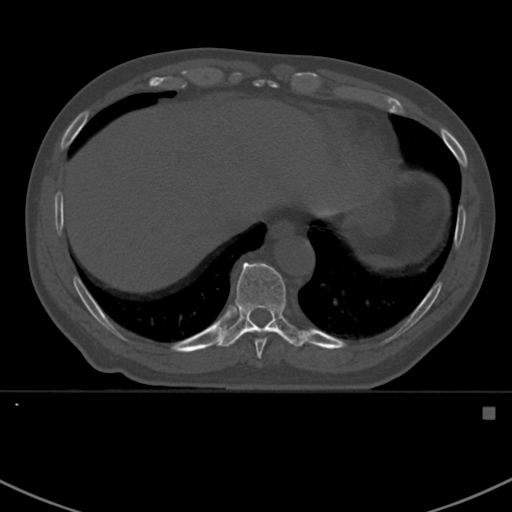
CT including the spine, one axial slice; slice 371 of 412 in the series (ordered by position); reconstruction kernel Br40s; bone window (W 1800 / L 400 HU); 1.5 mm slice thickness; 512 × 512 image matrix, field of view 358 × 358 mm. Patient: male, 59 years. Case-level facts recorded for this patient, not image findings: primary cancer: prostate.
Outlined on this slice (semi-automatically segmented with operator editing):
- T10 vertebra: bounding box [x1, y1, x2, y2] px = [216, 262, 305, 347]
- T9 vertebra: [255, 338, 266, 359]